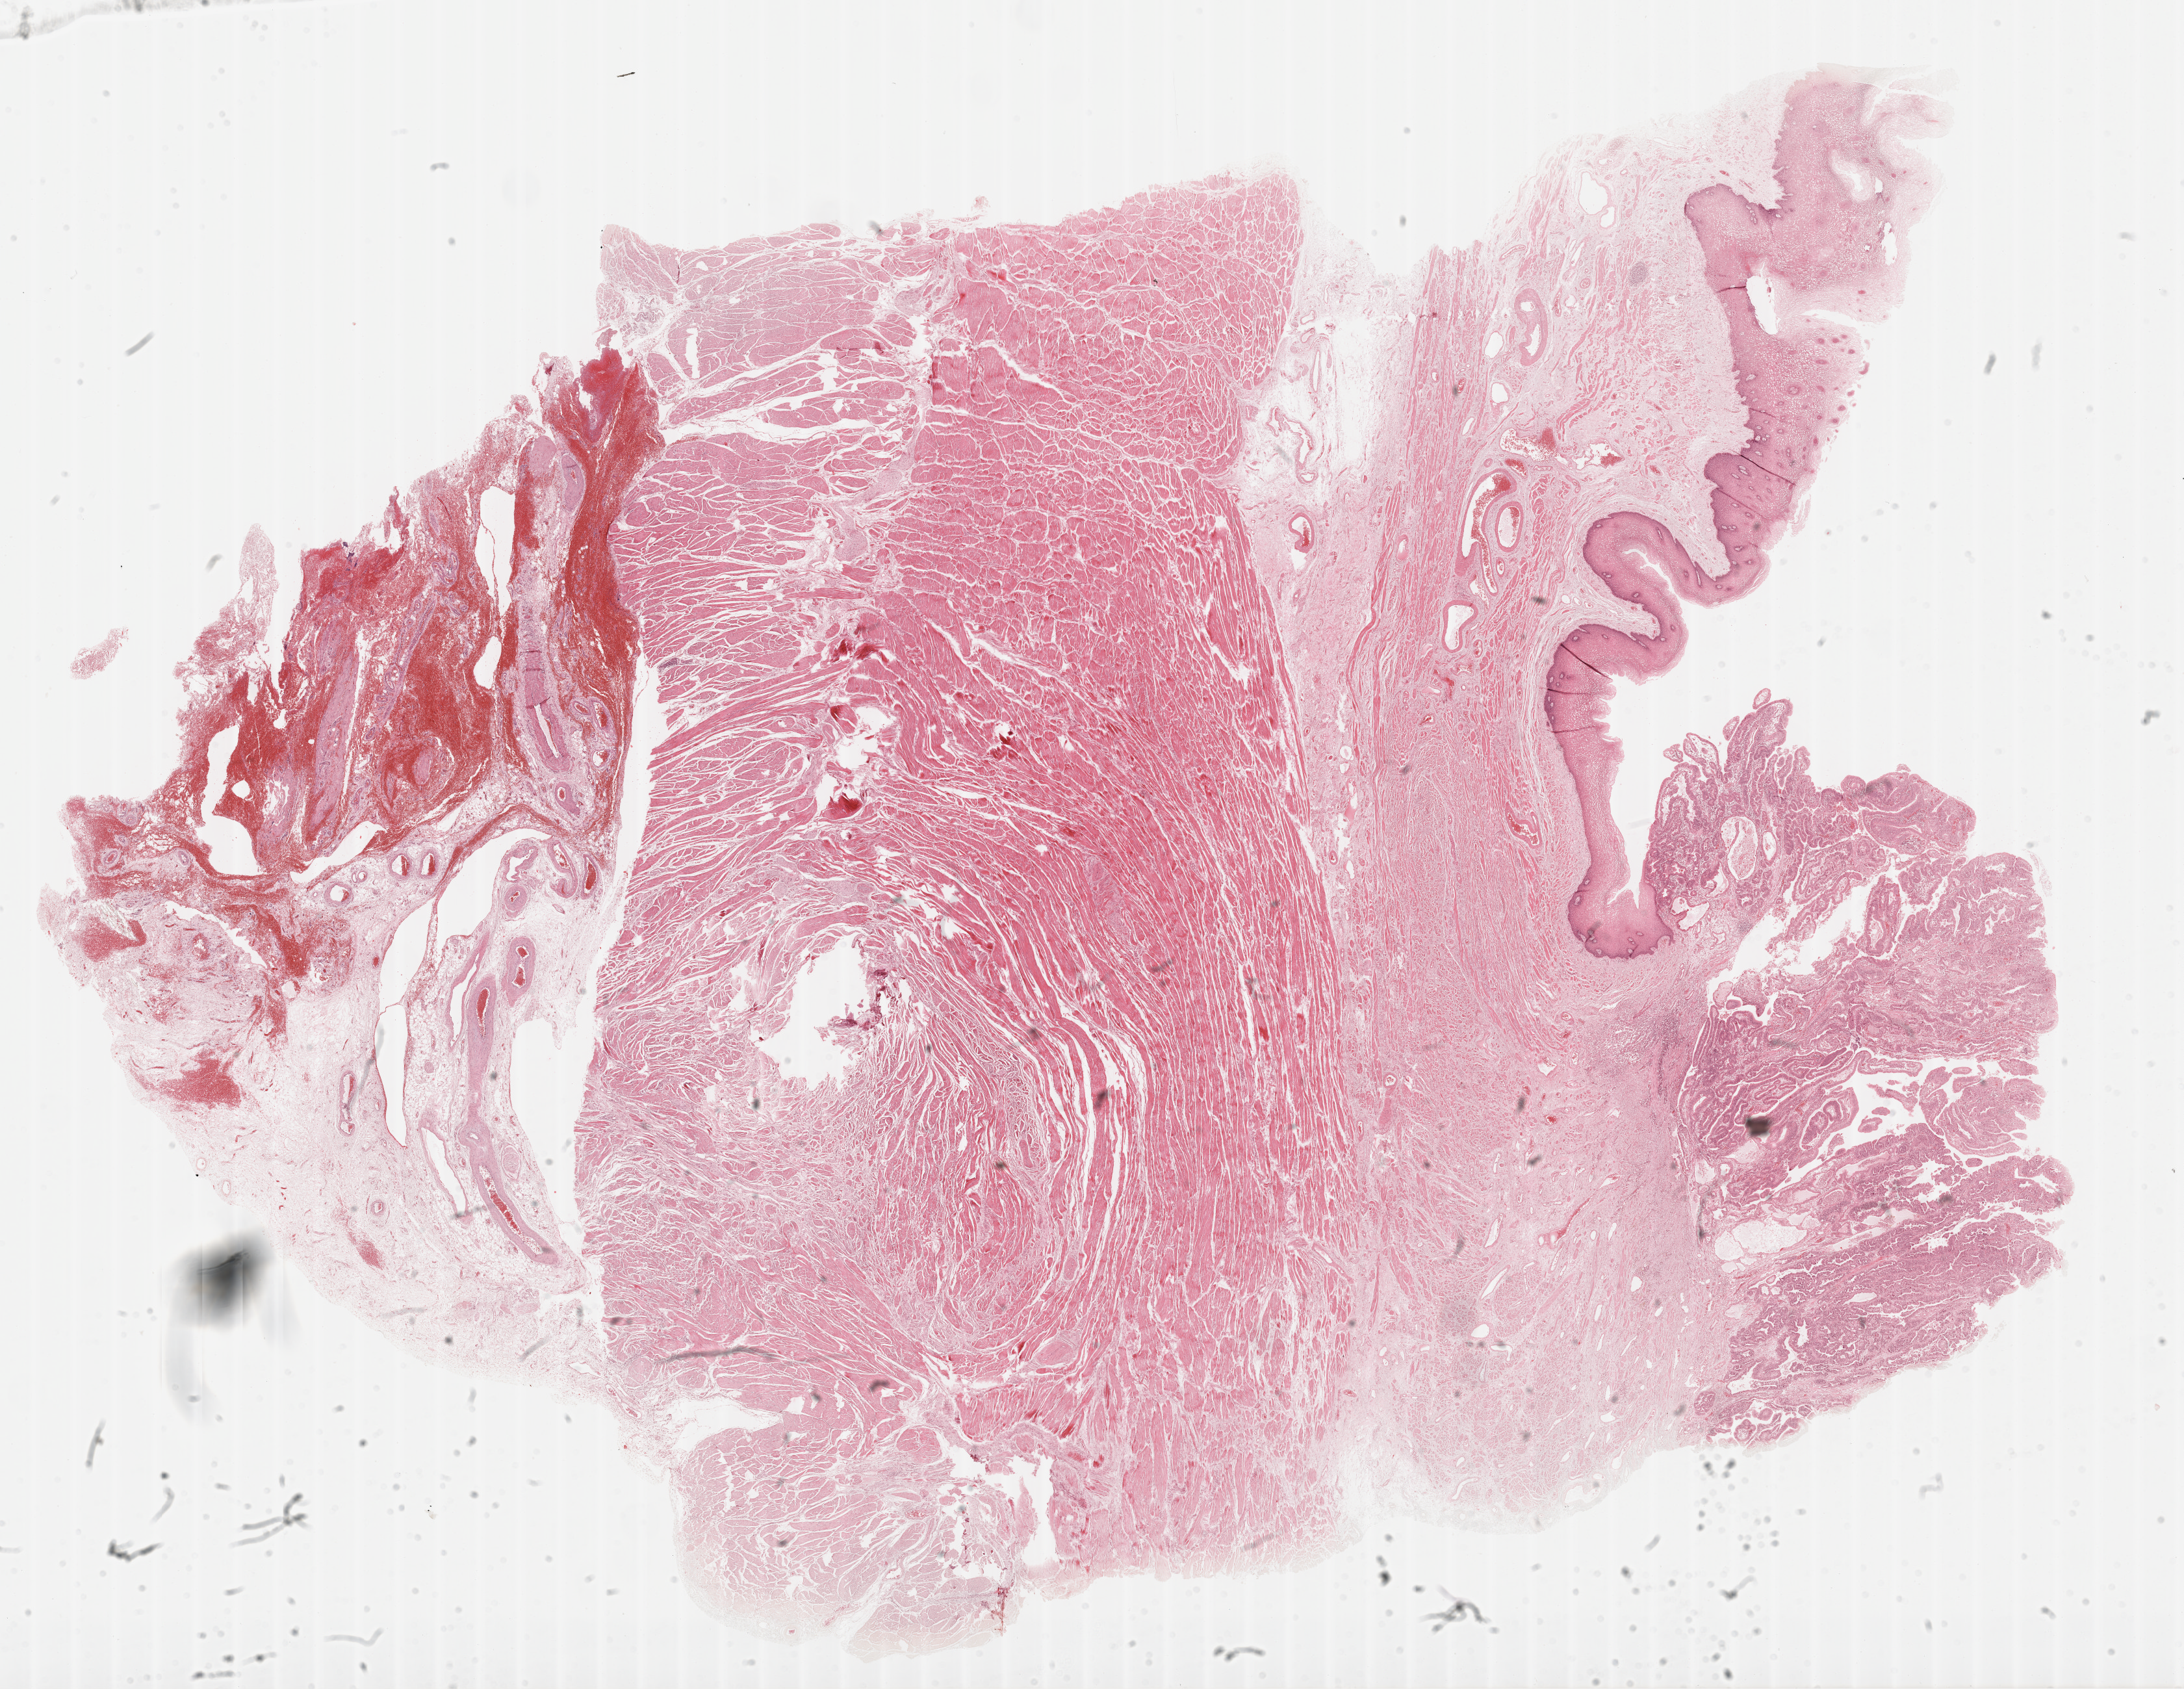
Hematoxylin and eosin (H&E) stained whole-slide image — a low-resolution overview of the entire scanned area, about 27.2 x 21.0 mm (slide scanned at 40x). Formalin-fixed paraffin-embedded (FFPE) diagnostic section. Esophagus, primary tumour sample. Male, age 57 years at initial diagnosis. Histologic grade: G2 (moderately differentiated).
AJCC pathologic stage: I. Lymph nodes positive (case pathology): 0 of 19 examined. Diagnosis: Adenocarcinoma, NOS (lower third of esophagus).